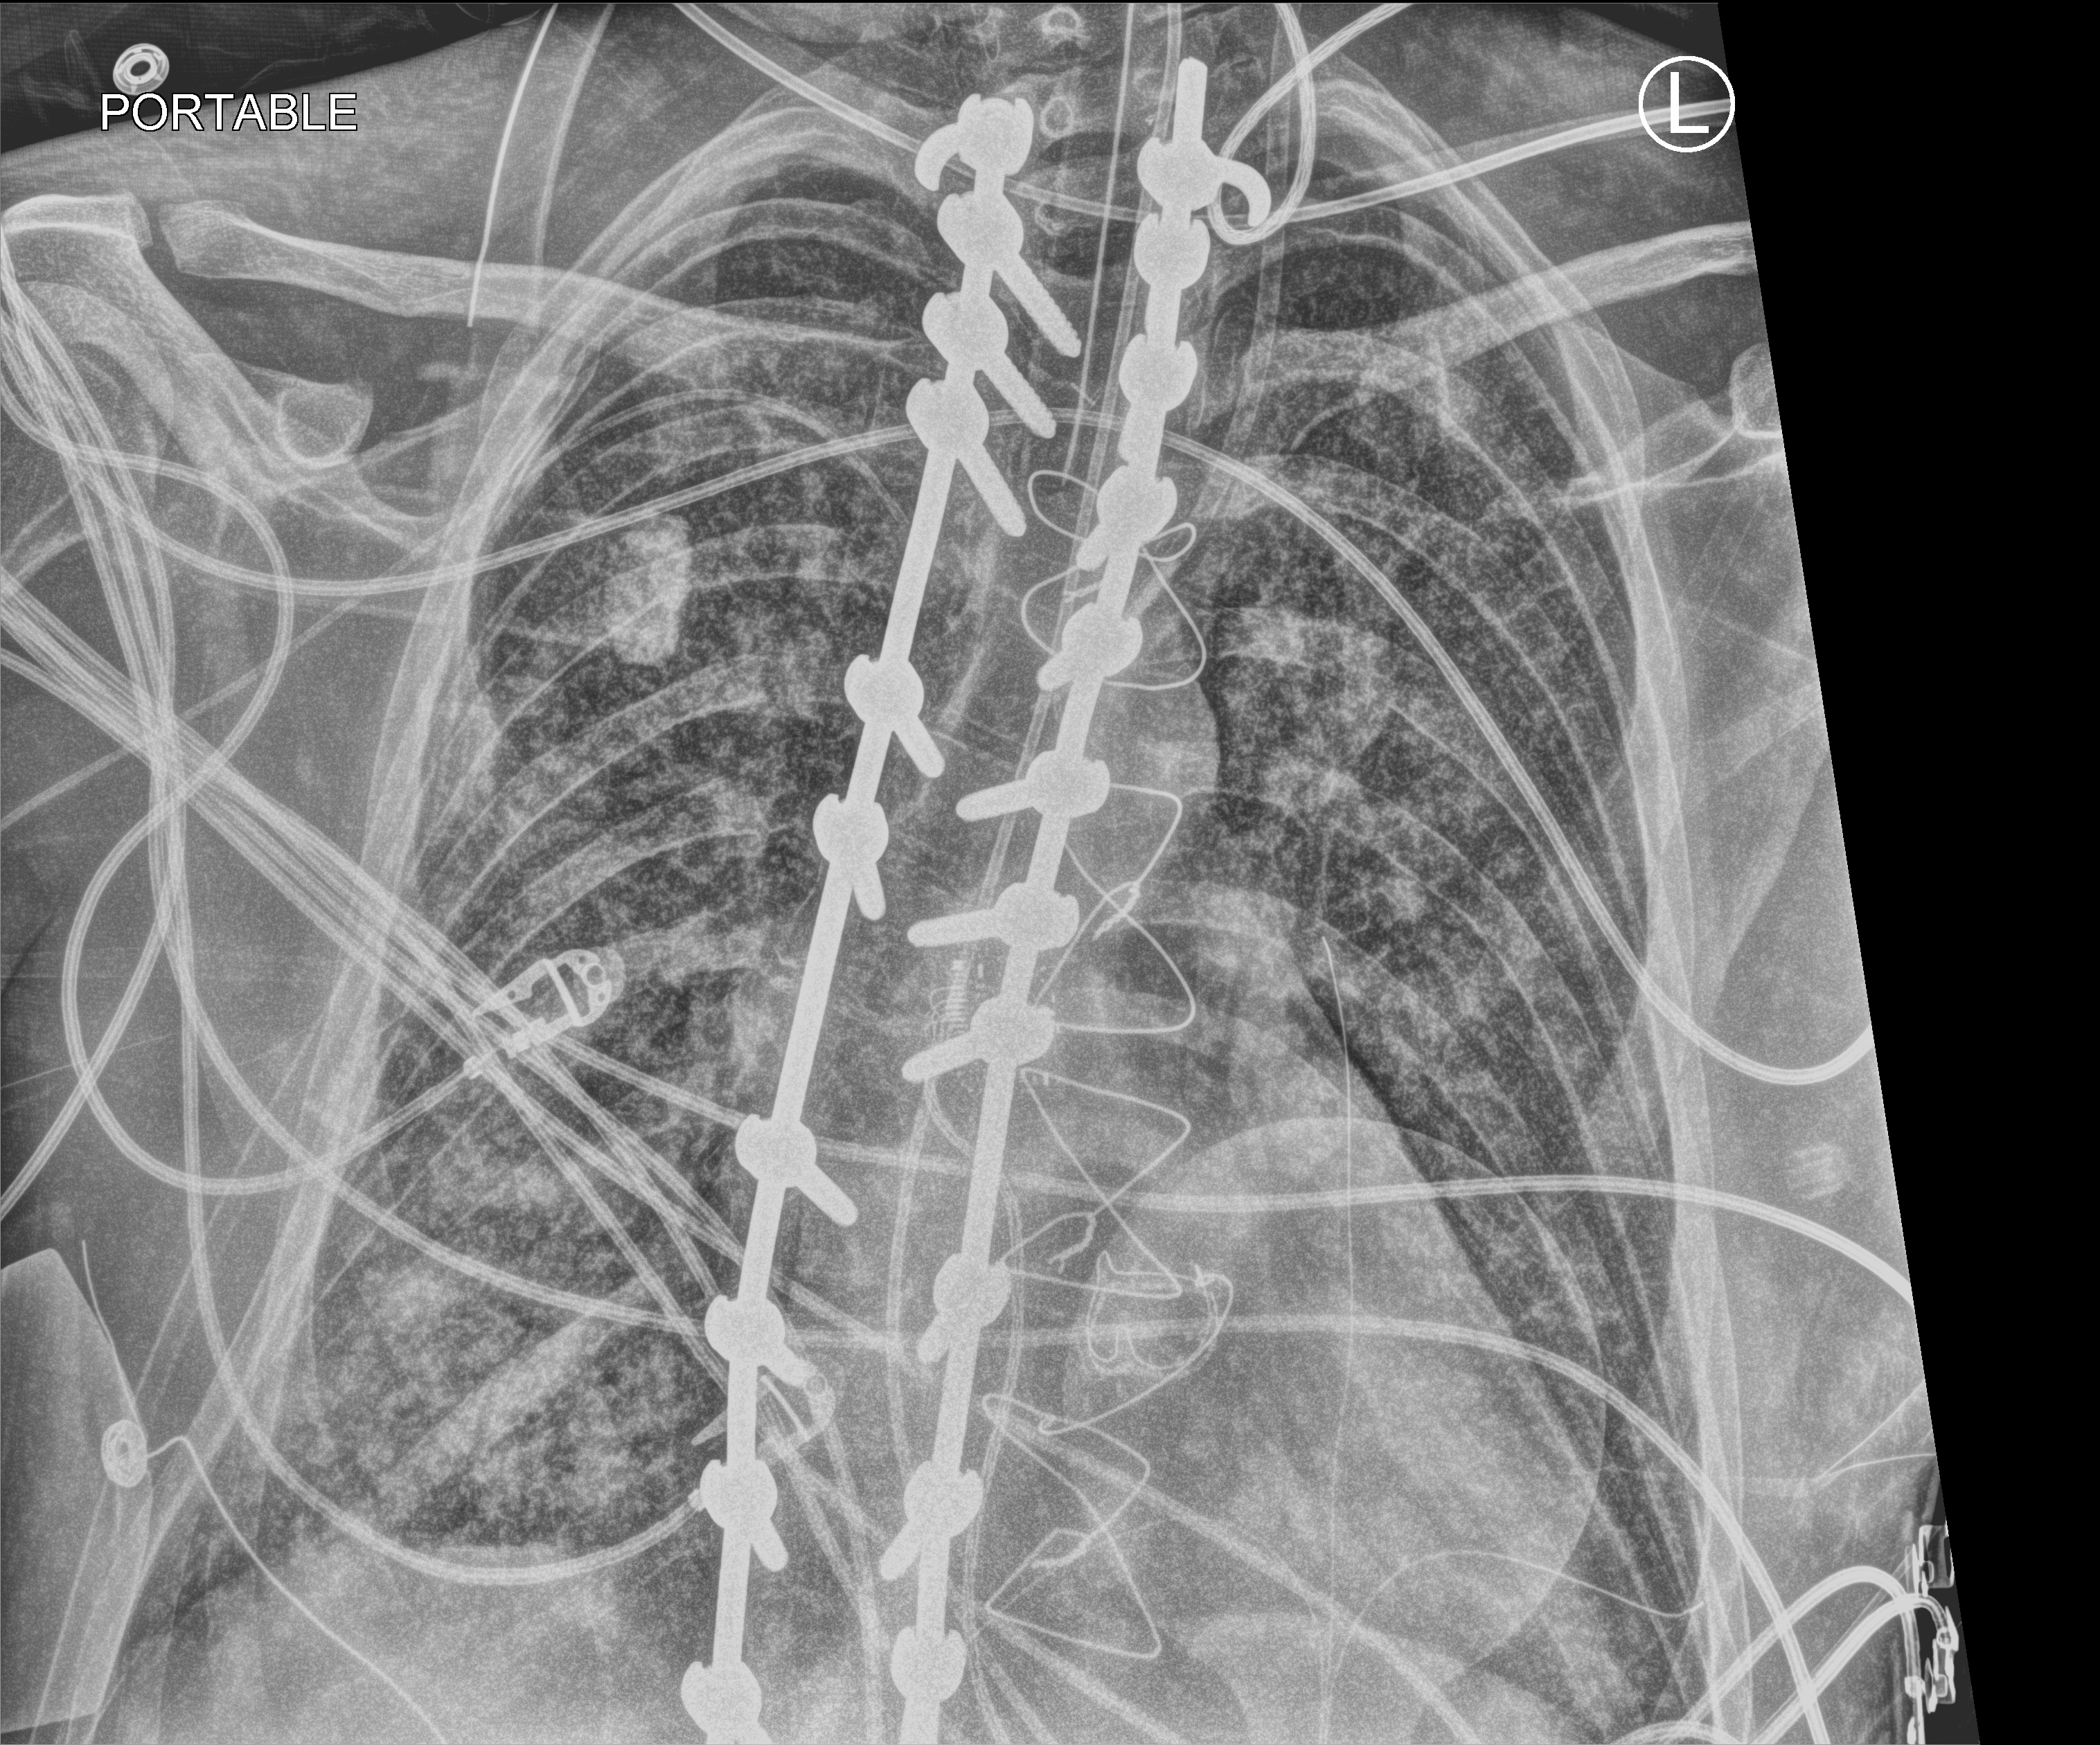
Portable chest radiograph, anteroposterior (AP) projection. Patient hospitalised with COVID-19, aged 18–59 years.
Hospital-stay facts (about this admission, not read from this image; timing relative to this image not recorded):
- chronic kidney disease (admission record): no
- admitted to intensive care during this hospital stay: yes
- length of hospital stay: 15 days